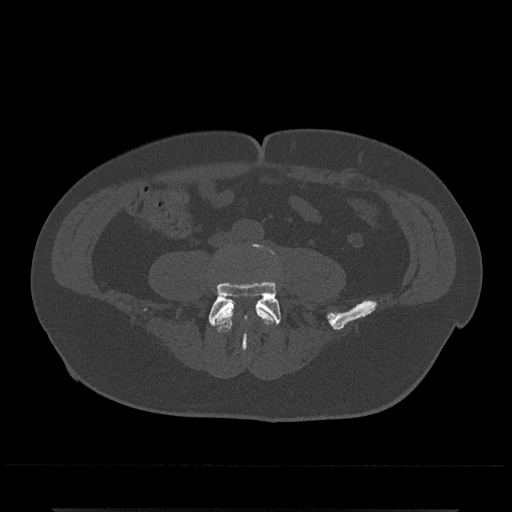
CT including the spine, one axial slice; slice 112 of 797 in the series (ordered by position); reconstruction kernel Br40s/3; 120 kVp; bone window (W 1800 / L 400 HU); 0.5 mm slice thickness; 512 × 512 image matrix. Male patient, age 67 years. From the clinical record (not read from this slice): primary cancer: prostate.
Outlined on this slice (semi-automatic segmentation, software-assisted and operator-edited):
- L4 vertebra: bounding box <212,301,278,332> (left, top, right, bottom; pixels)
- L5 vertebra: <208,243,281,350>